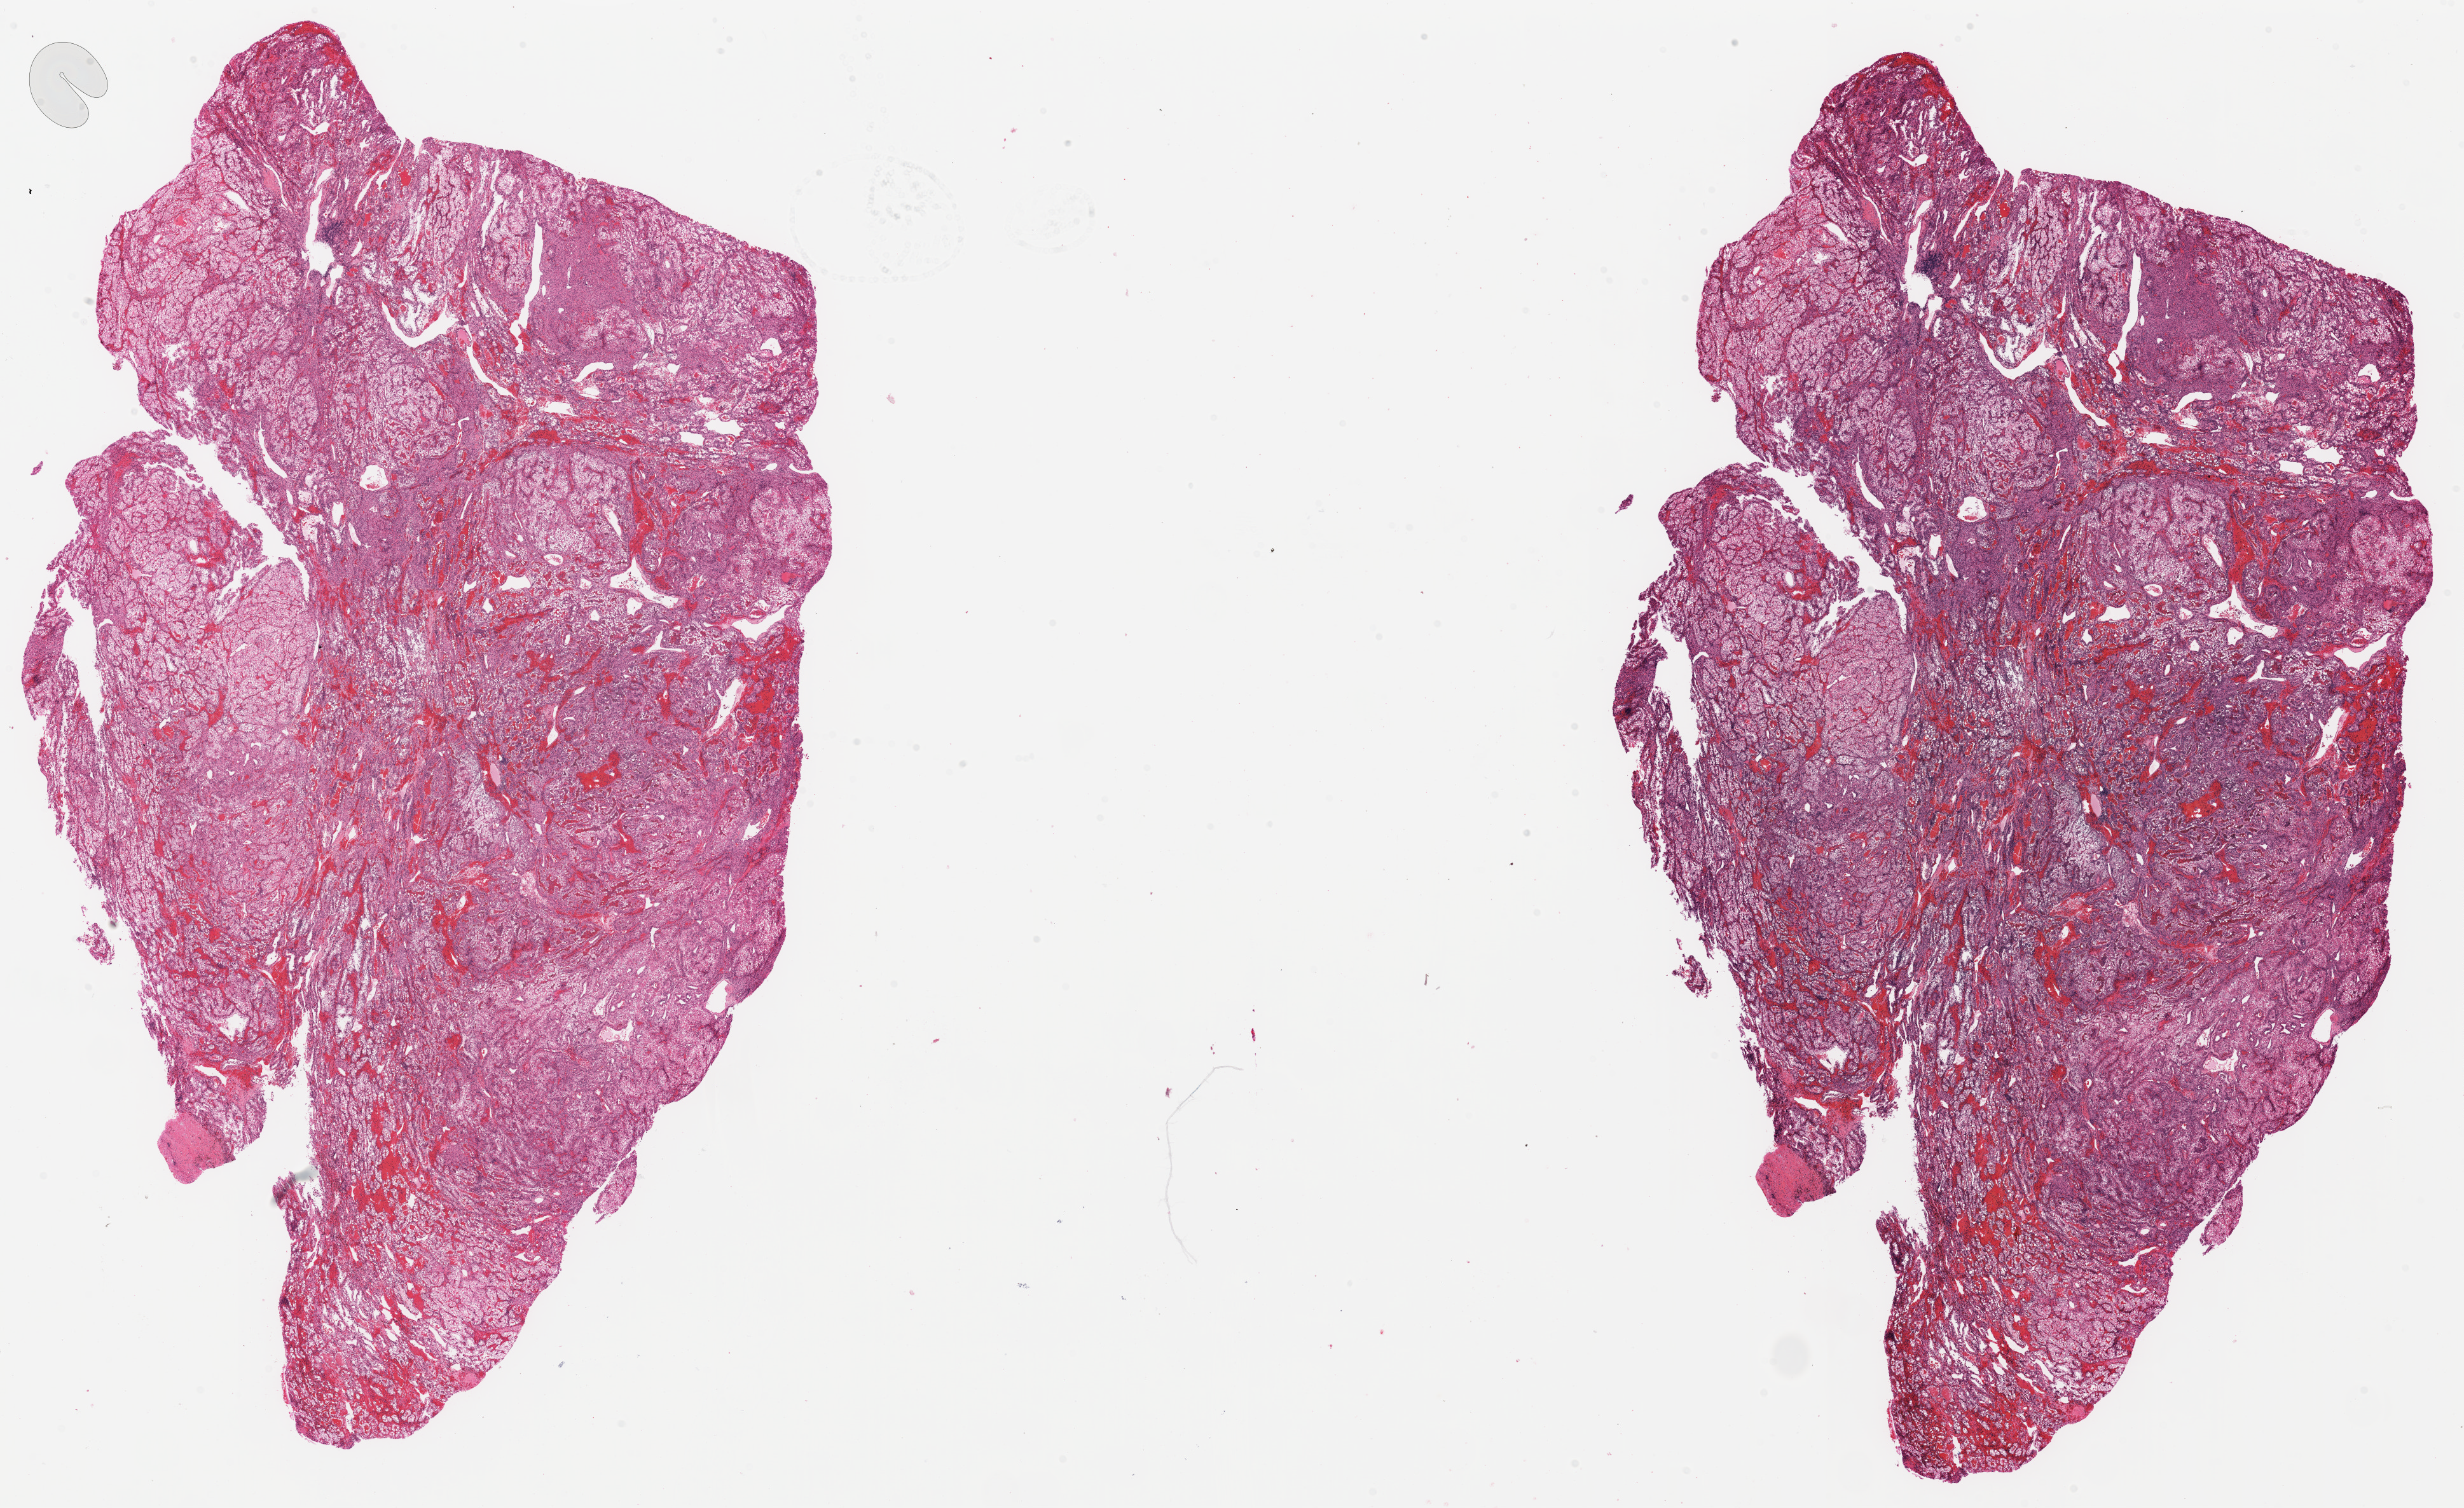
Digitized Hematoxylin and eosin (H&E) stained tissue section (whole slide) — whole scanned area (about 30.6 x 18.8 mm, acquisition: 20x scan) shown as a low-resolution overview. FFPE section. Primary tumour sample from the kidney. Patient: male, age at initial diagnosis 65 years. Histologic grade: G3 (poorly differentiated).
Pathologic diagnosis: Clear cell adenocarcinoma, NOS. Laterality: right. AJCC pathologic stage: III (7th edition).